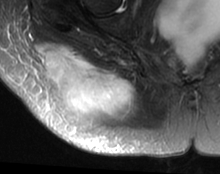
MRI of an extremity soft-tissue mass, one axial slice. Position 18 of 63 along the scan axis. T2-weighted fat-saturated. MR volume resampled by the dataset authors to the PET/CT grid (not the native acquisition matrix). 3.27 mm slice thickness. 220 × 174 image matrix. Female patient. From the clinical record (not read from this slice): histological type: spindle cell suggestive of myxofibrosarcoma; grade: intermediate; site of the primary tumour: right buttock.
Structures marked on this image (expert contour drawn on MRI and transferred to this co-registered scan by the dataset authors):
- gross tumour volume (mass): box from (x=38, y=43) to (x=137, y=131) px